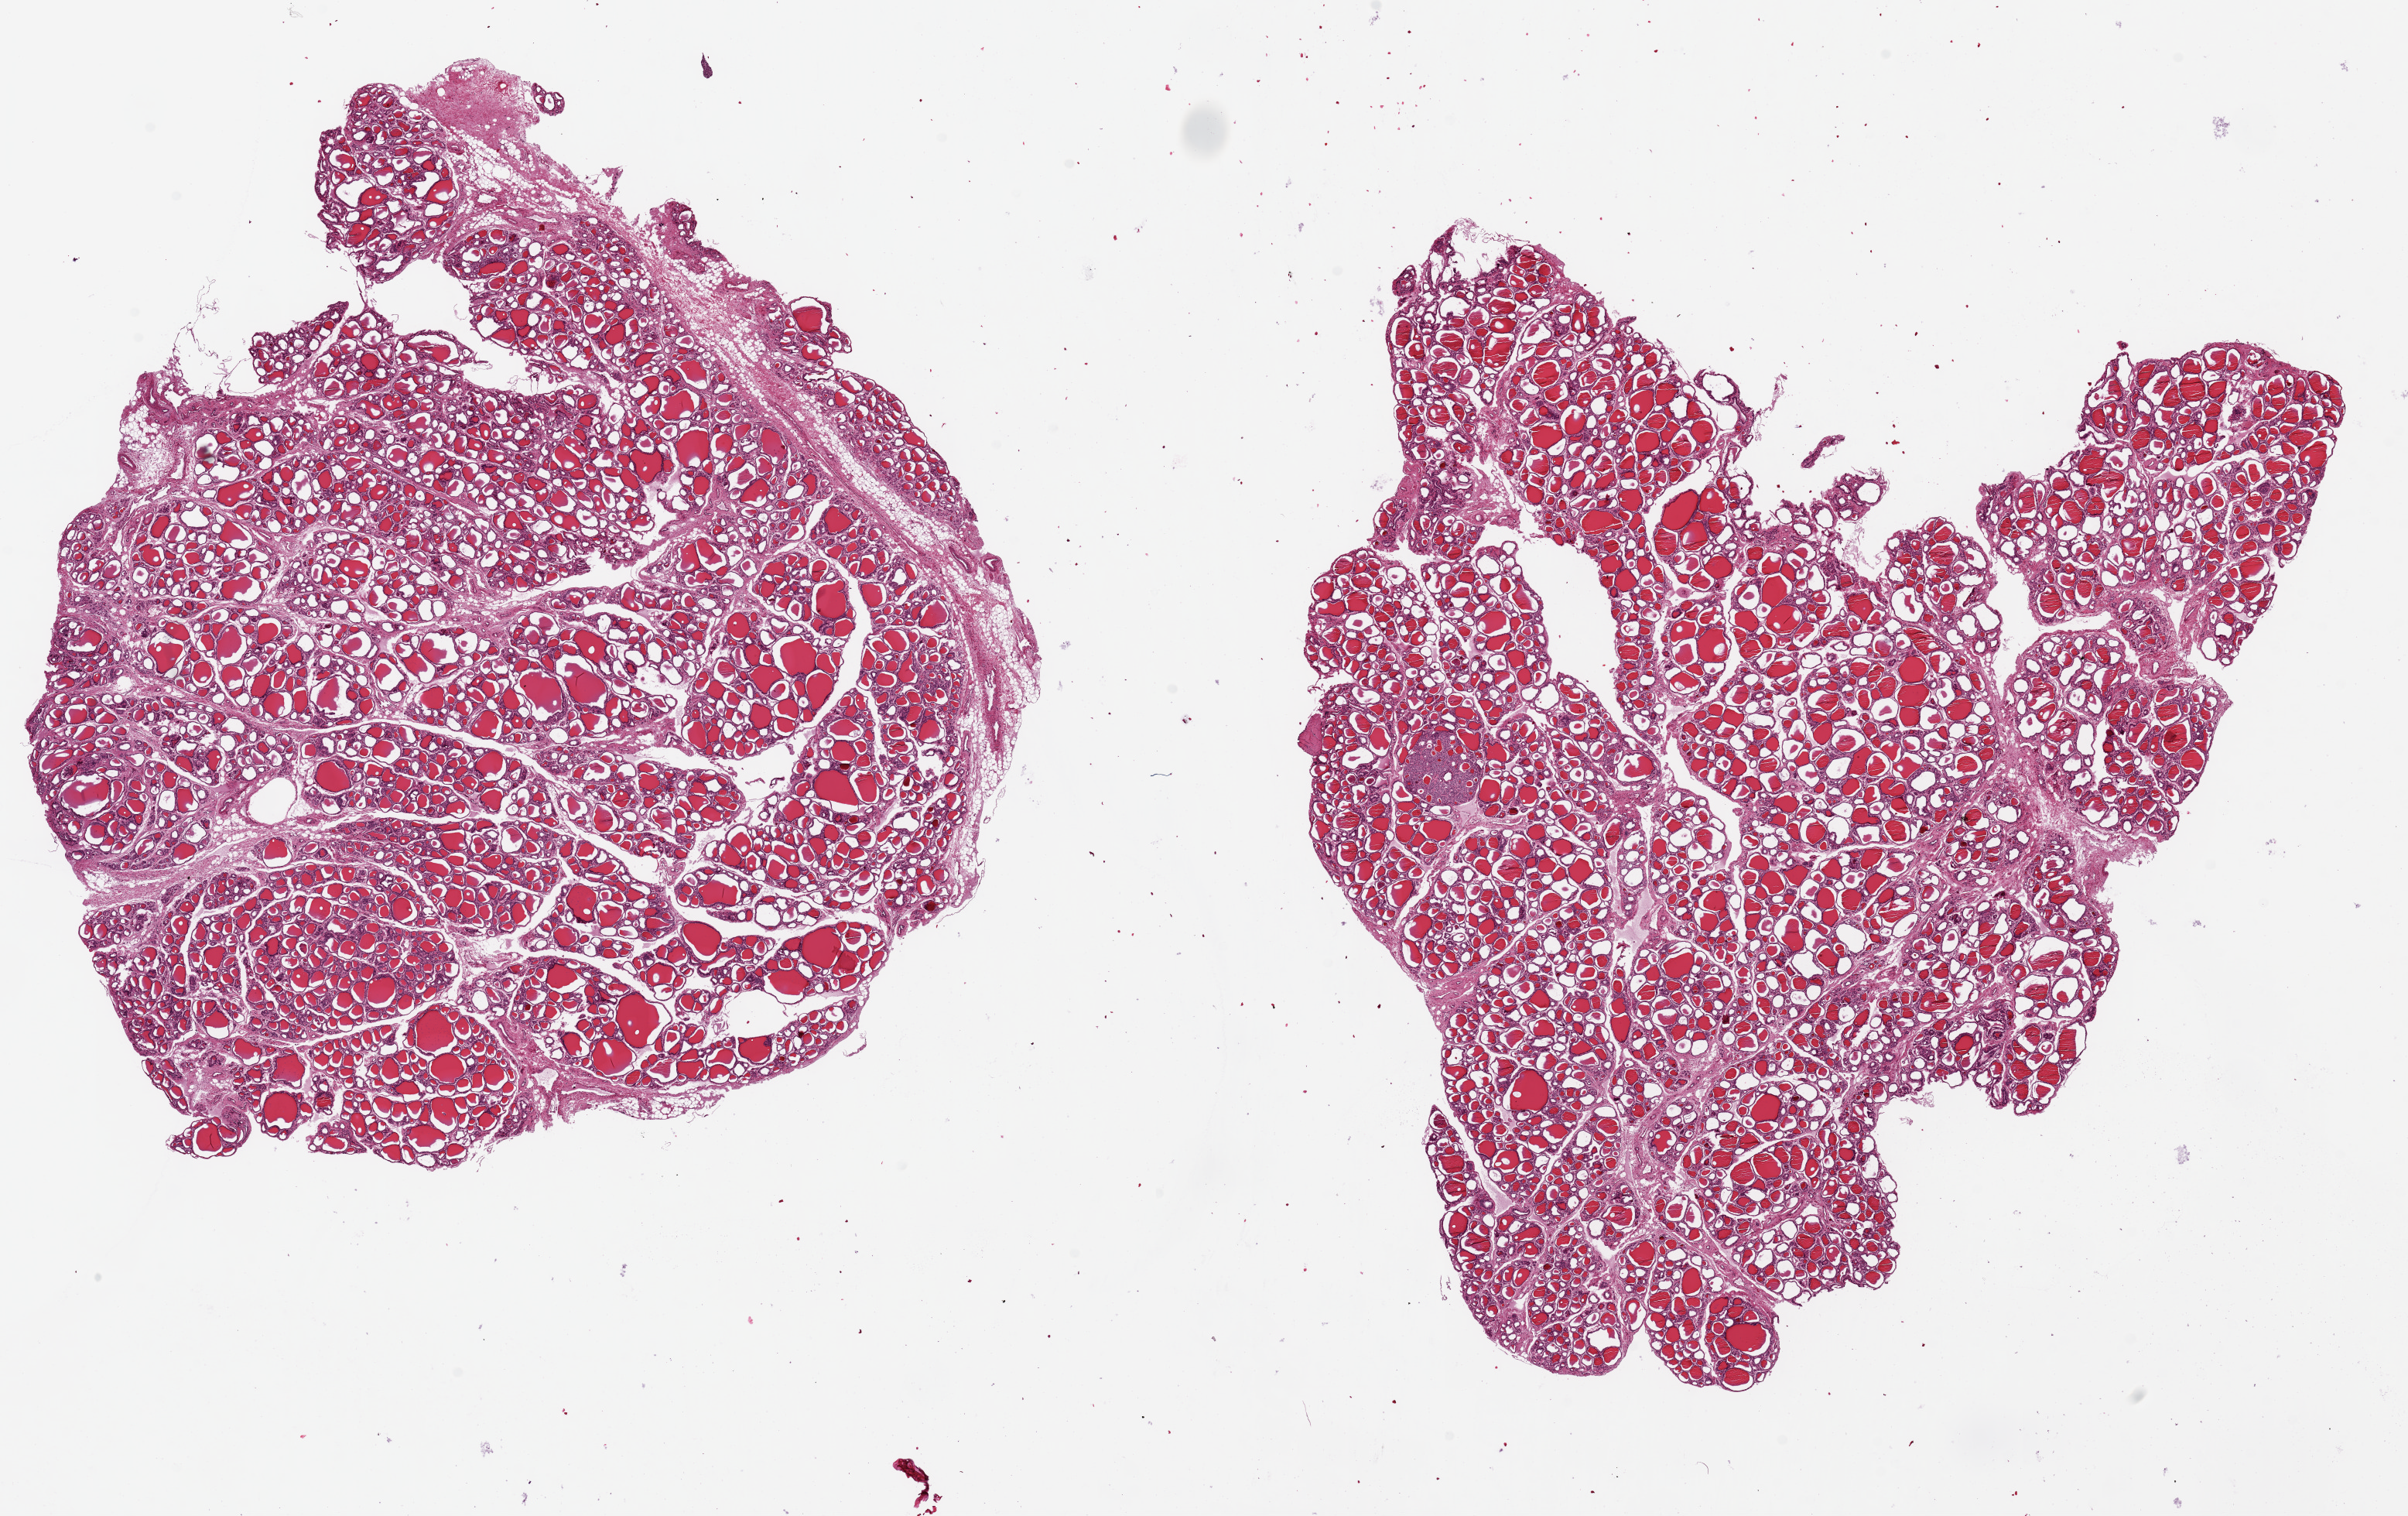
Whole-slide image, H&E stain, brightfield, low-resolution overview of the scanned area, about 24.6 x 15.5 mm (from a 20x scan); PAXgene-fixed paraffin-embedded (PFPE) section; sampled site (target tissue): thyroid; tissue donor sample. Donor sex: male.
• reviewer comment on this tissue sample: 2 pieces ~12x8mm, early multinodular goiter